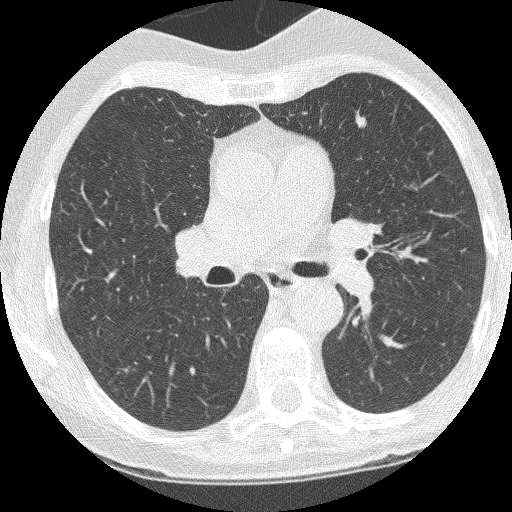
Axial slice from a low-dose chest CT screening exam, third annual screen, lung window (W 1500 / L -600 HU), 1.25 mm slice thickness, lung (sharp) reconstruction kernel (BONE), 512 × 512 image matrix. Female, age 60 years at enrolment. Current smoker at enrolment.
Expert reader's lesion annotation, bounding box (x1, y1, x2, y2) in pixels: (345, 112, 375, 141). The screening reader recorded 2 non-calcified nodules or masses ≥4 mm on this exam (left upper lobe, left upper lobe); which of them this box marks is not recorded. Lung cancer was diagnosed 37 days after this screen: adenocarcinoma, NOS, left upper lobe, moderately differentiated (G2), stage IA (AJCC 6th edition), 6 mm at pathology.